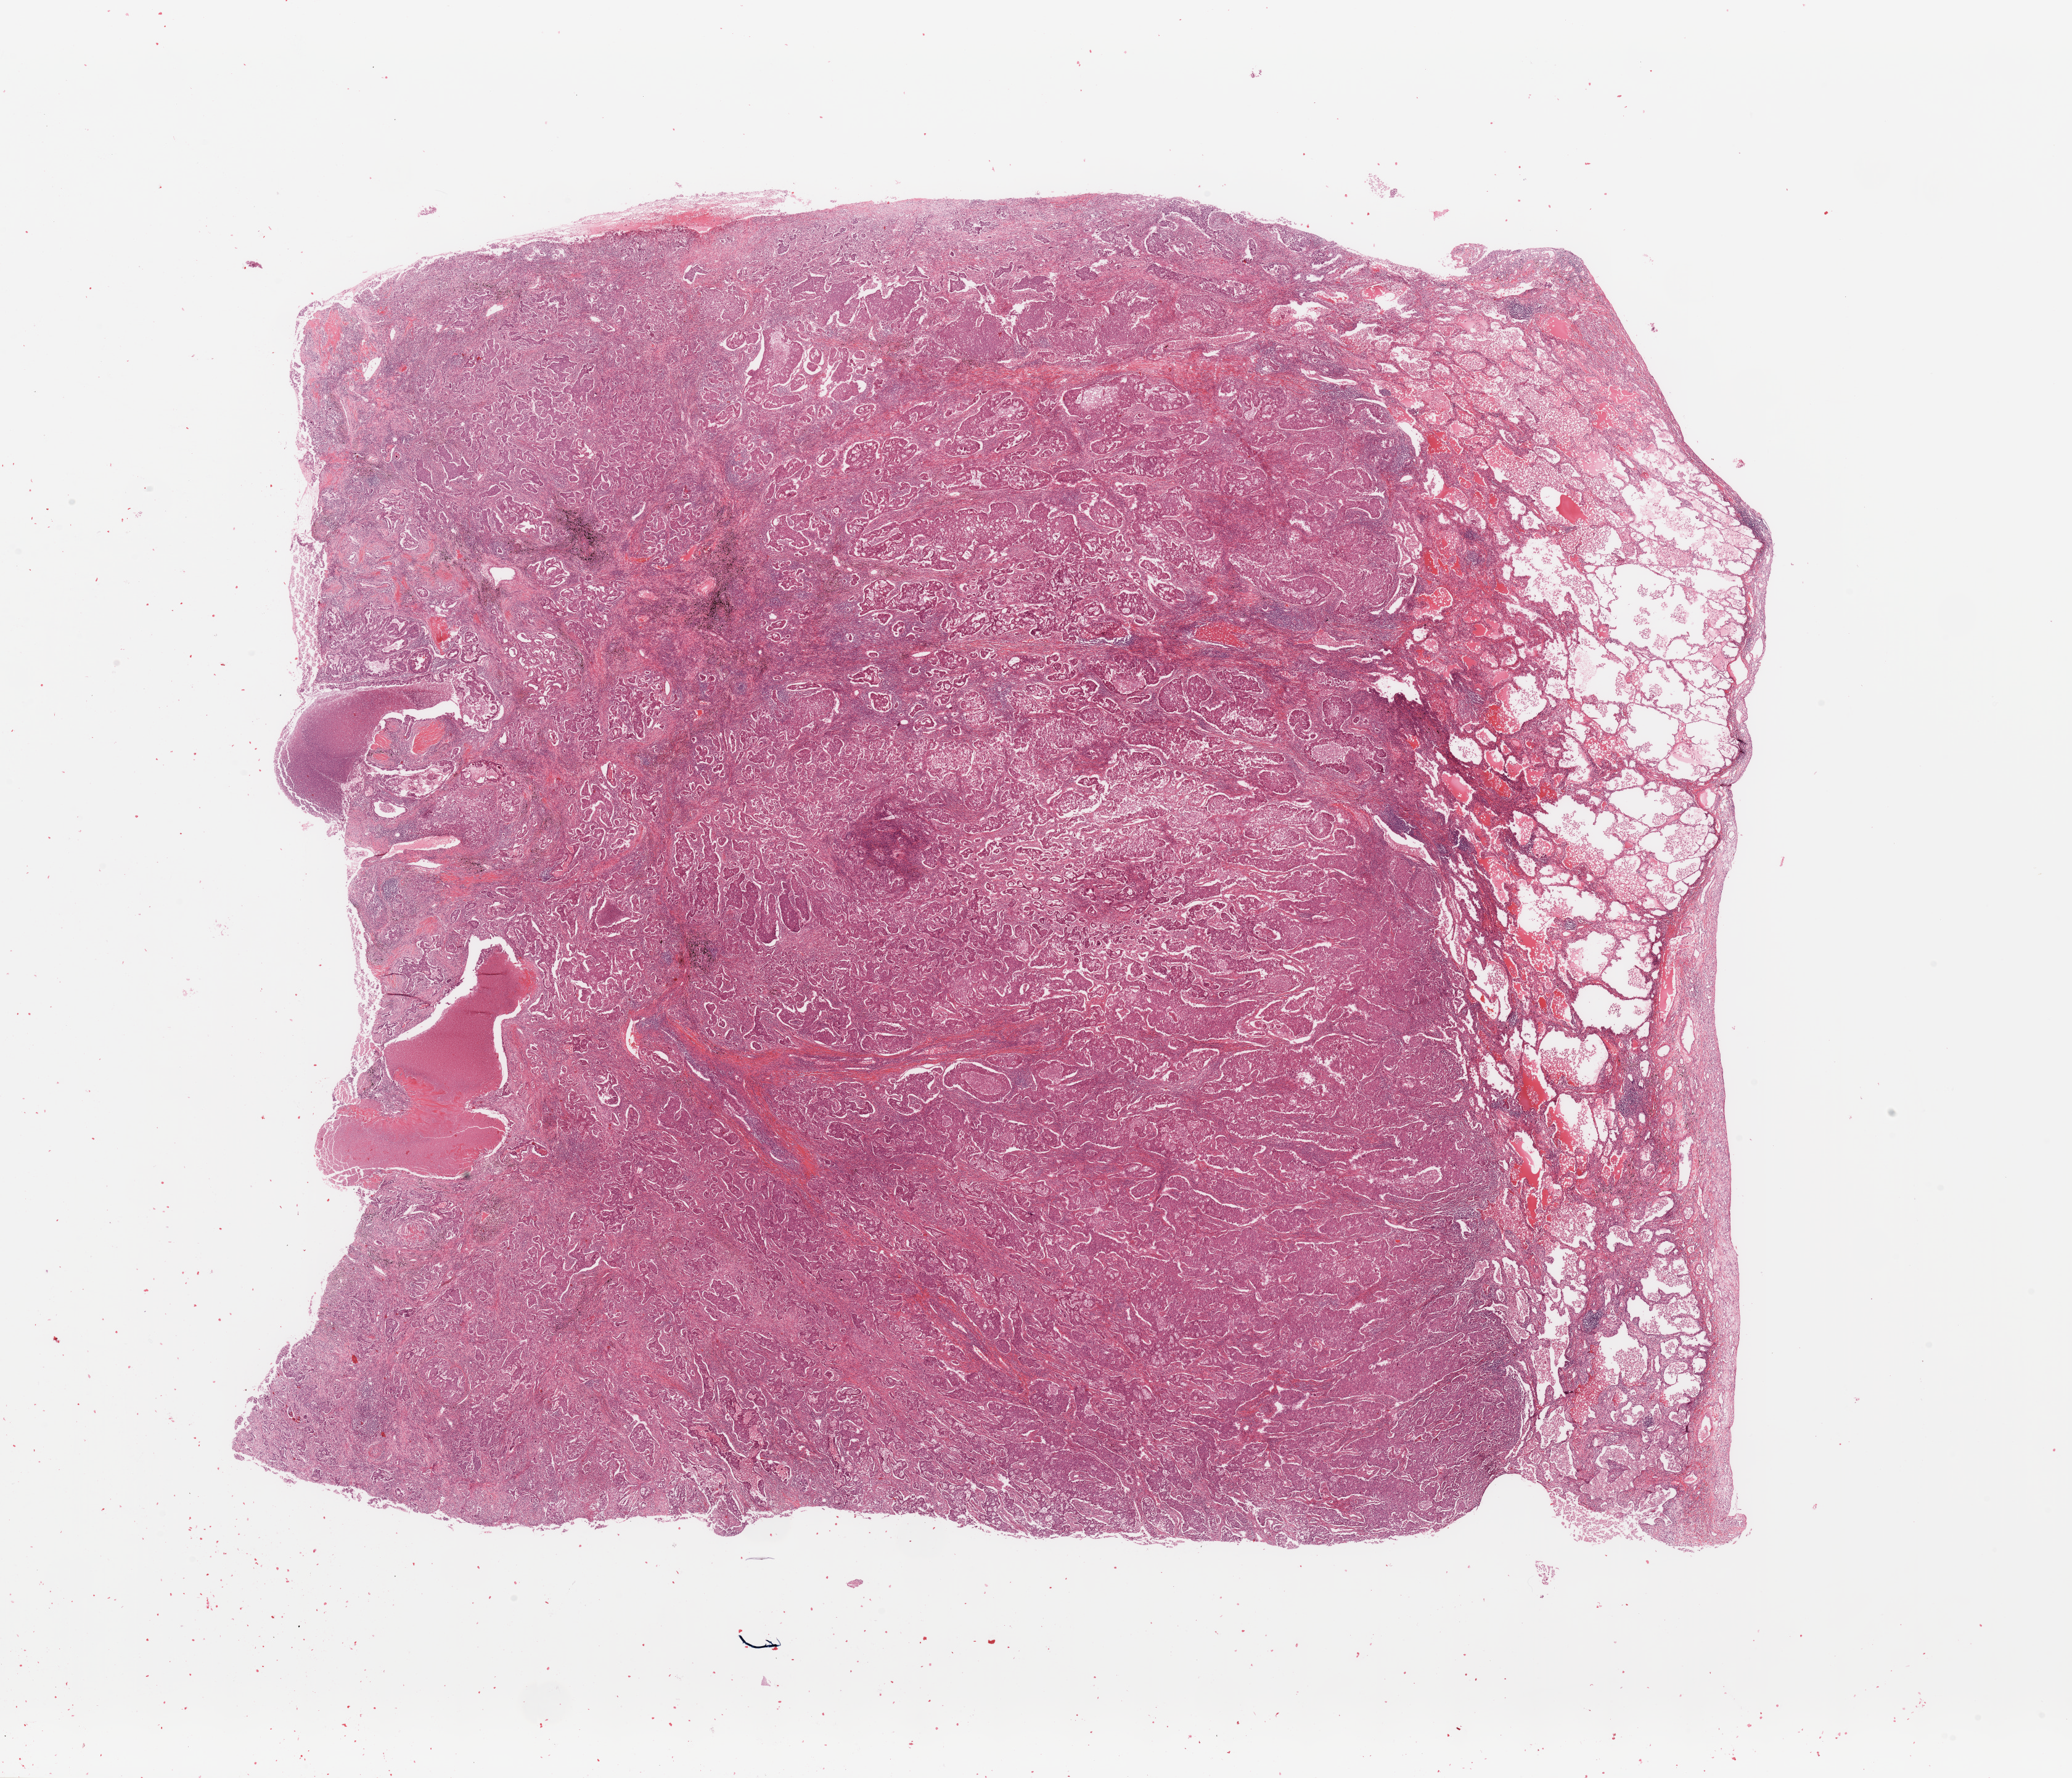
Digitized H&E tissue section (whole slide), whole scanned area (about 26.6 x 22.8 mm) shown as a low-resolution overview. Lung, tumour tissue. 49-year-old male patient. Histologic grade: G3 (poorly differentiated).
Diagnosis: Adenocarcinoma, NOS. AJCC pathologic stage: IIB.